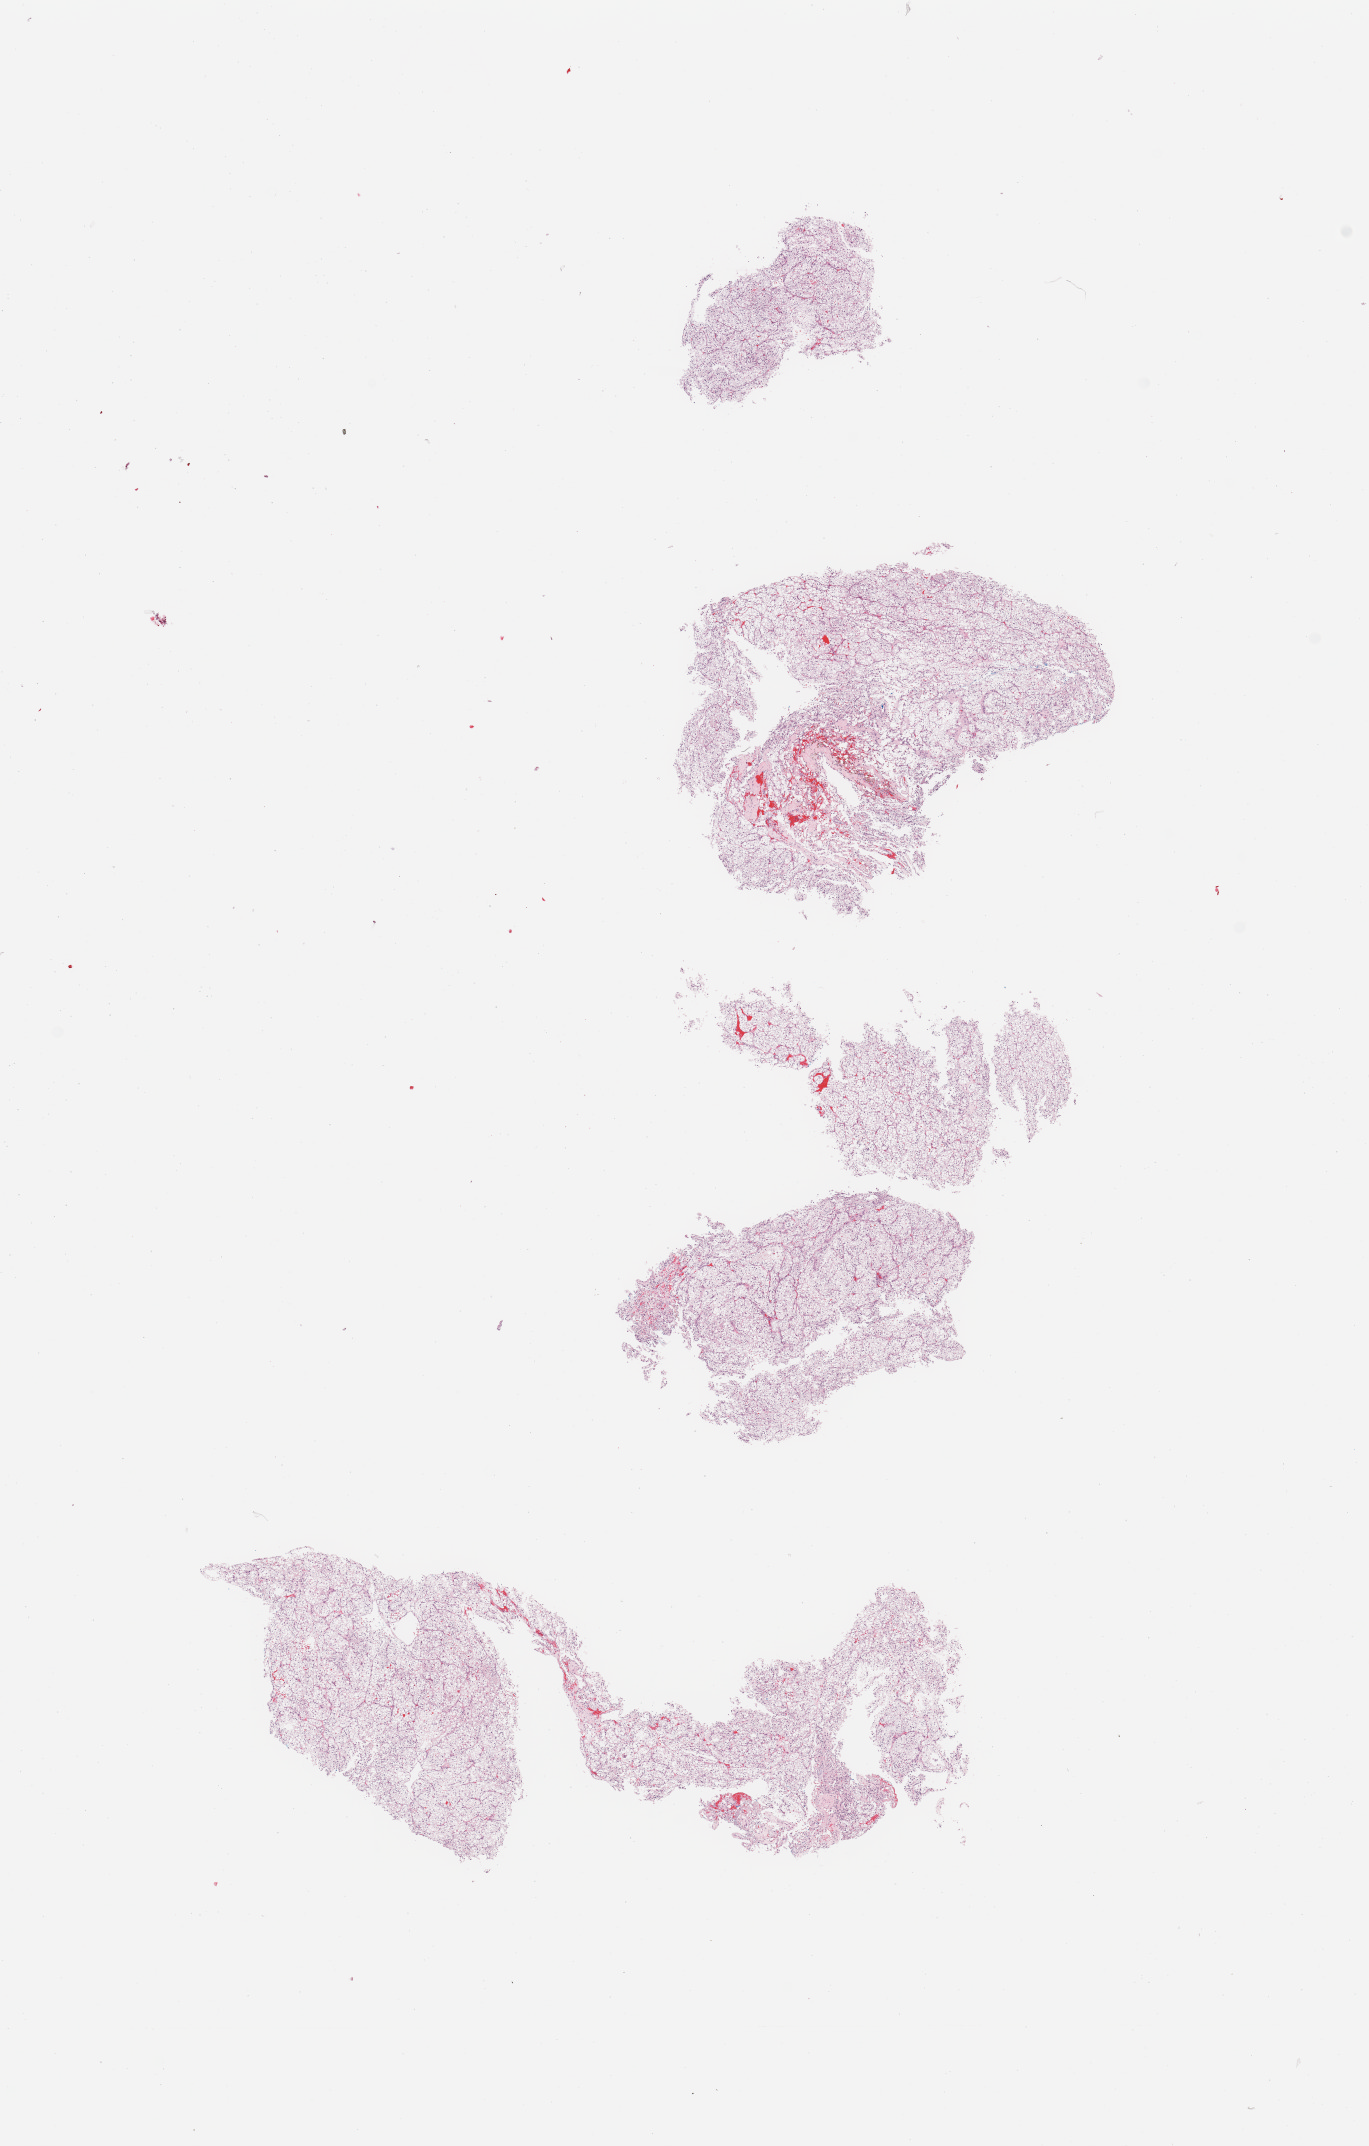
Digitized H&E-stained tissue section (whole slide) — a low-resolution overview of the entire scanned area, about 10.8 x 17.0 mm, tumour tissue sample, sampled site: kidney. Male, 57 y/o. Histologic grade: G1 (well differentiated). Slide review estimates, as recorded: tumour nuclei 95%, necrosis 0%.
- AJCC pathologic stage: I
- primary tumour site (as recorded): lower pole
- diagnosis: Renal cell carcinoma, NOS